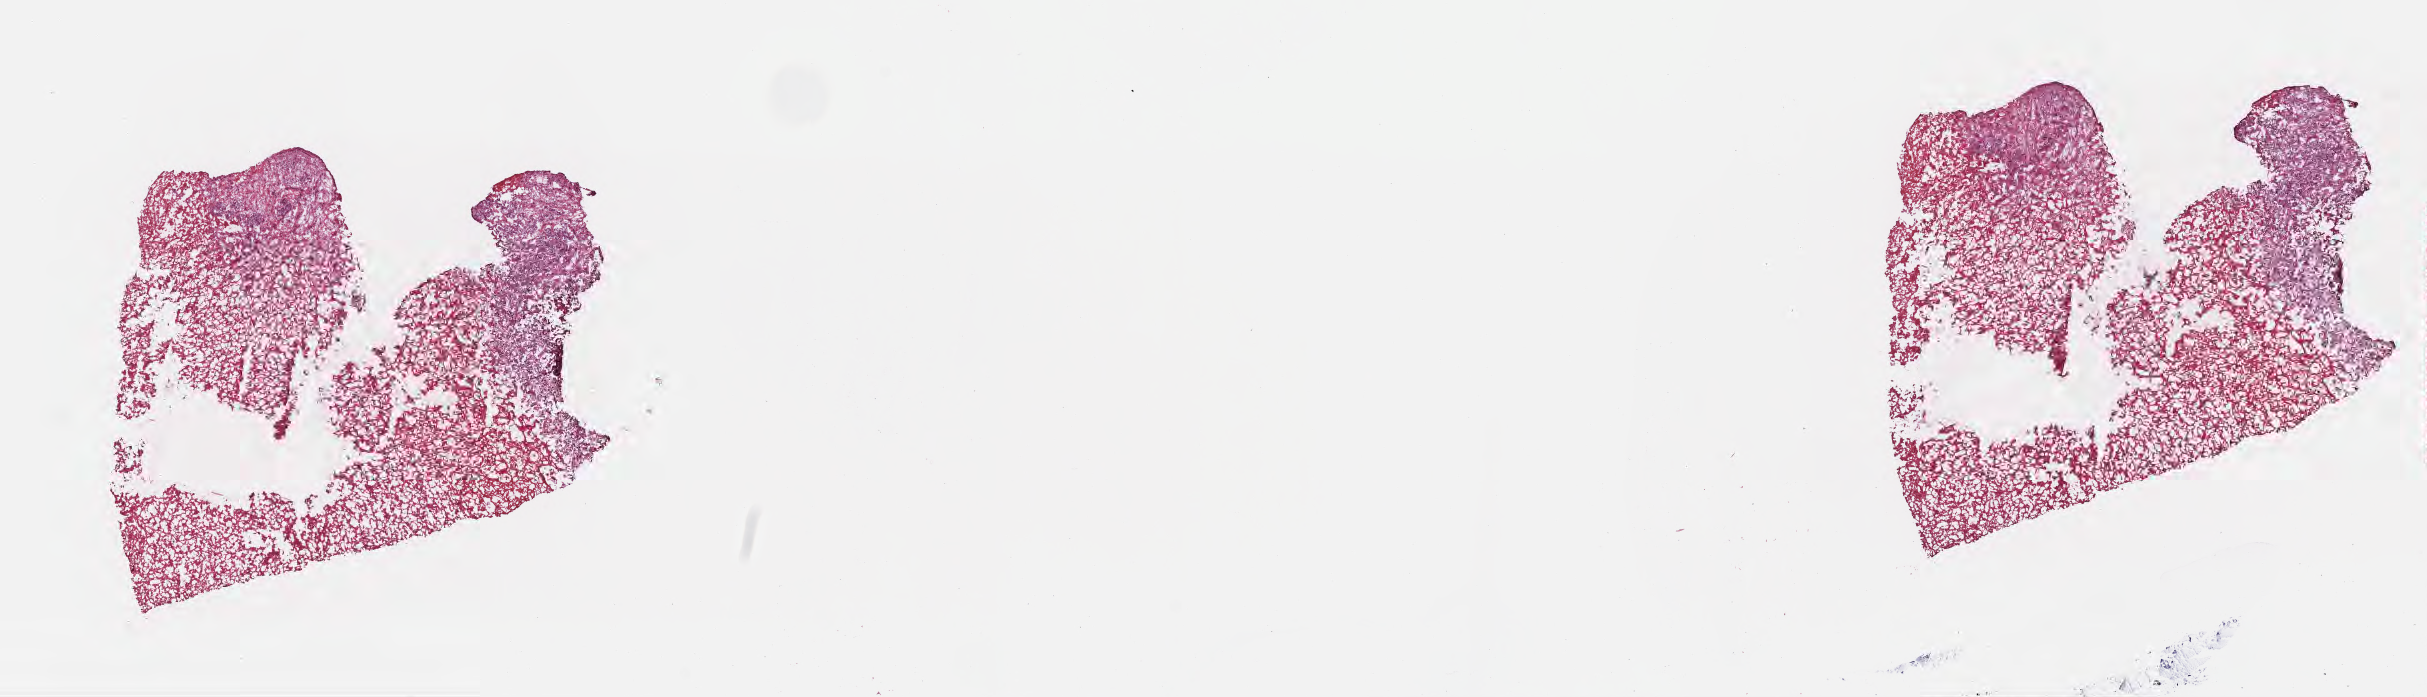
Digitized hematoxylin and eosin (H&E)-stained section, low-resolution overview of the scanned area, about 19.6 x 5.6 mm; cryosection; primary tumor; site: breast. Female patient; age at initial diagnosis 46 years. Tumor grade: G3 (poorly differentiated). Pathologist review of this section (percent, as recorded): tumor cells 30%, tumor nuclei 40%, stromal cells 20%, necrosis 0%, normal cells 50%. Inflammatory infiltration, as recorded: lymphocyte infiltration 0%, monocyte infiltration 0%, neutrophil infiltration 0%.
AJCC pathologic stage: Stage IIB. Histologic diagnosis: Metaplastic carcinoma, NOS.